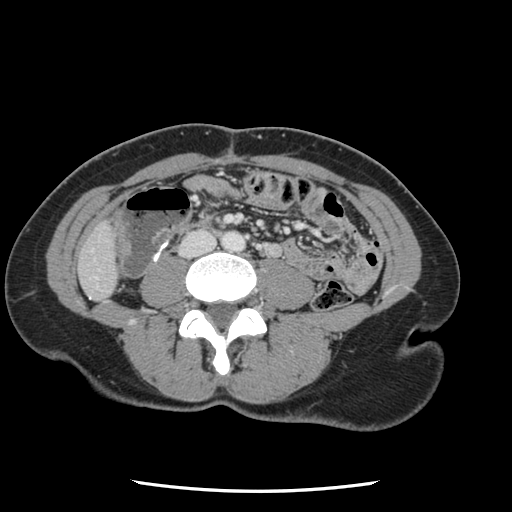
Contrast-enhanced abdominal CT, one axial slice; slice 5 of 134 in the series (ordered by position); 120 kVp; intravenous contrast given; soft-tissue window (W 400 / L 40 HU); 512 × 512 image matrix. Female patient, age 43 years. From the clinical record (not read from this slice): diagnosis: colorectal cancer liver metastases, imaged before liver resection; multiple liver metastases: yes; largest metastasis: 3.4 cm.
Annotated regions visible in this slice (expert manual segmentation):
- liver: bounding box (x1, y1, x2, y2) in pixels: (80, 225, 117, 300)
- planned liver remnant (the part of the liver to remain after resection): (80, 225, 117, 301)